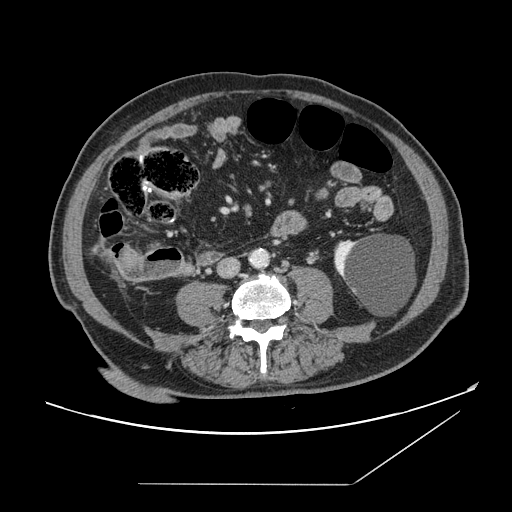
Contrast-enhanced abdominal CT, one axial slice; slice 20 of 166 in the series (ordered by position); 120 kVp; intravenous contrast given; soft-tissue window (W 400 / L 40 HU); 512 × 512 image matrix, field of view 416 × 416 mm. Male patient, age 80 years. Case-level facts recorded for this patient, not image findings: diagnosis: colorectal cancer liver metastases, imaged before liver resection; multiple liver metastases: no; largest metastasis: 2.2 cm.
Structures marked on this image (outlined manually by an expert reader):
- liver: bounding box (x1, y1, x2, y2) in pixels: (119, 249, 139, 271)